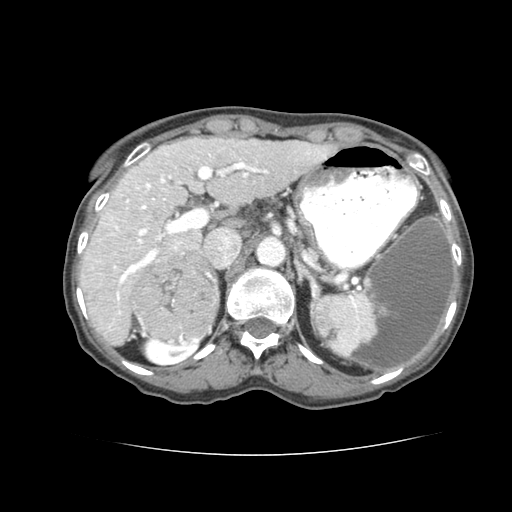
Contrast-enhanced abdominal CT (liver protocol), one axial slice; position 48 of 77 along the scan axis; reconstruction kernel STANDARD; 120 kVp; soft-tissue window (W 400 / L 40 HU); 2.5 mm slice thickness; 512 × 512 image matrix. Case-level facts recorded for this patient, not image findings: diagnosis: hepatocellular carcinoma (patient treated with transarterial chemoembolisation; whether this scan precedes or follows treatment is not stated here); TNM stage (as recorded): Stage-I; Child-Pugh class: A; tumour differentiation: well differentiated; tumour nodularity: uninodular.
Structures marked on this image (semi-automatically segmented with operator editing):
- liver parenchyma outside the tumour (the mass and vessels are separate outlines, so this box may not span the whole liver): bounding box <78,136,342,342> (left, top, right, bottom; pixels)
- mass: <132,253,219,343>
- liver vessels: <84,145,268,315>